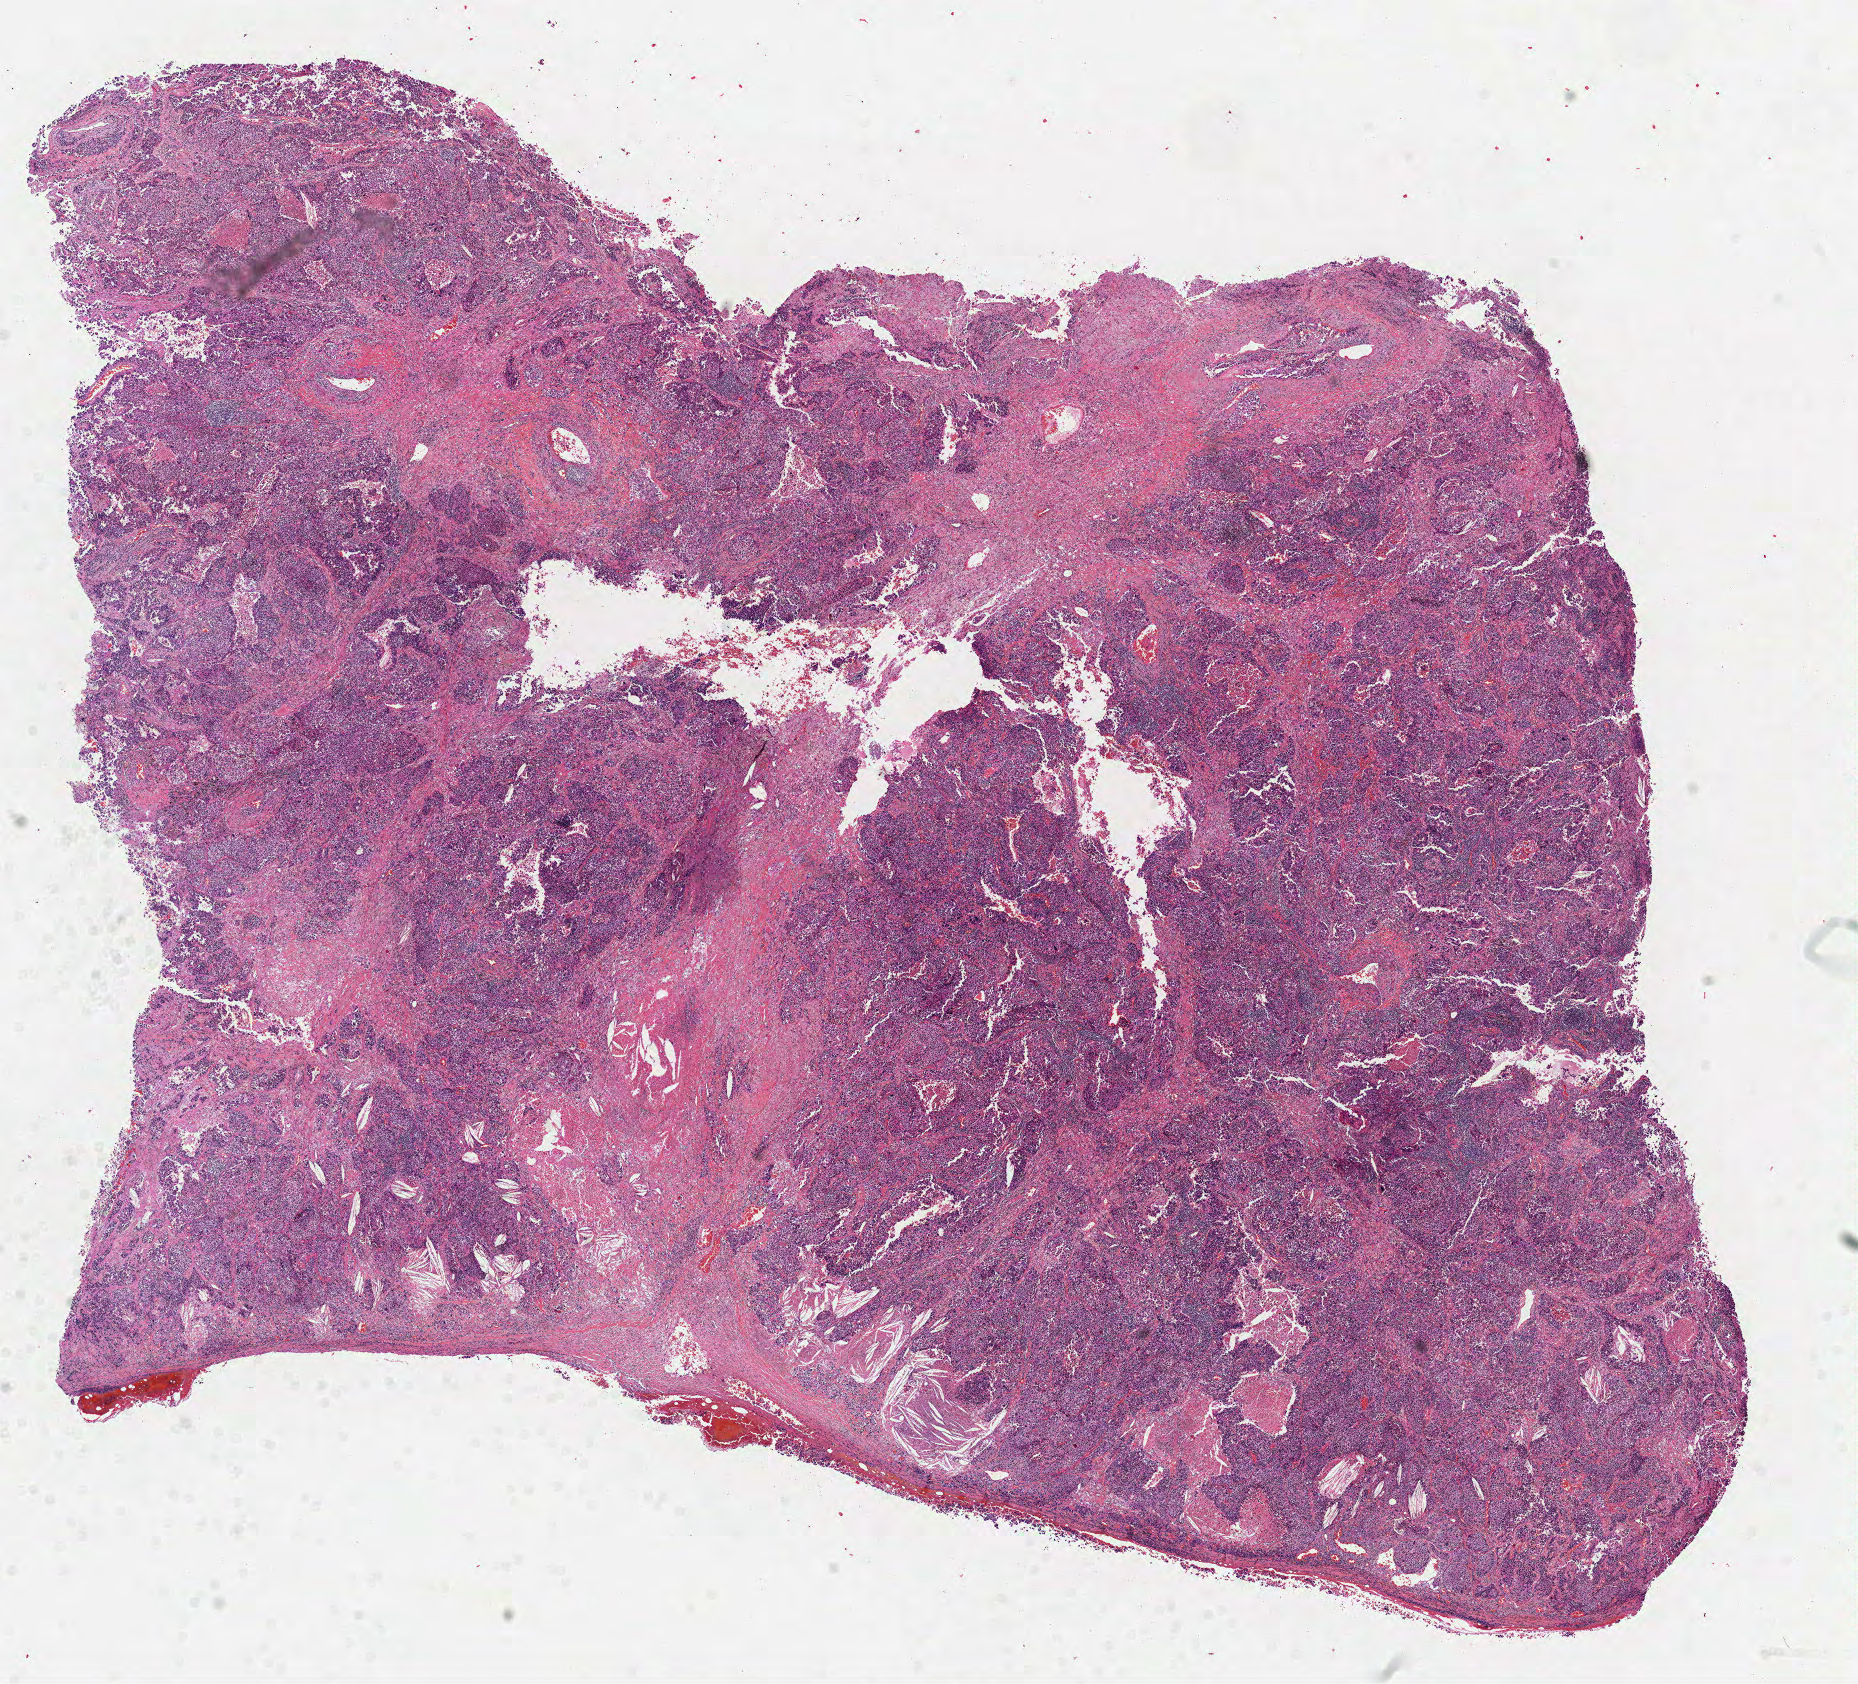
Whole-slide histology image, Hematoxylin and eosin (H&E) stained, low-resolution overview of the scanned area, about 15.0 x 13.6 mm; formalin-fixed paraffin-embedded (FFPE) diagnostic section; lung, primary tumour sample. Male patient; age at initial diagnosis 61 years.
Laterality: left. Pathologic diagnosis: Adenocarcinoma, NOS (upper lobe, lung). AJCC pathologic stage: IIIA.